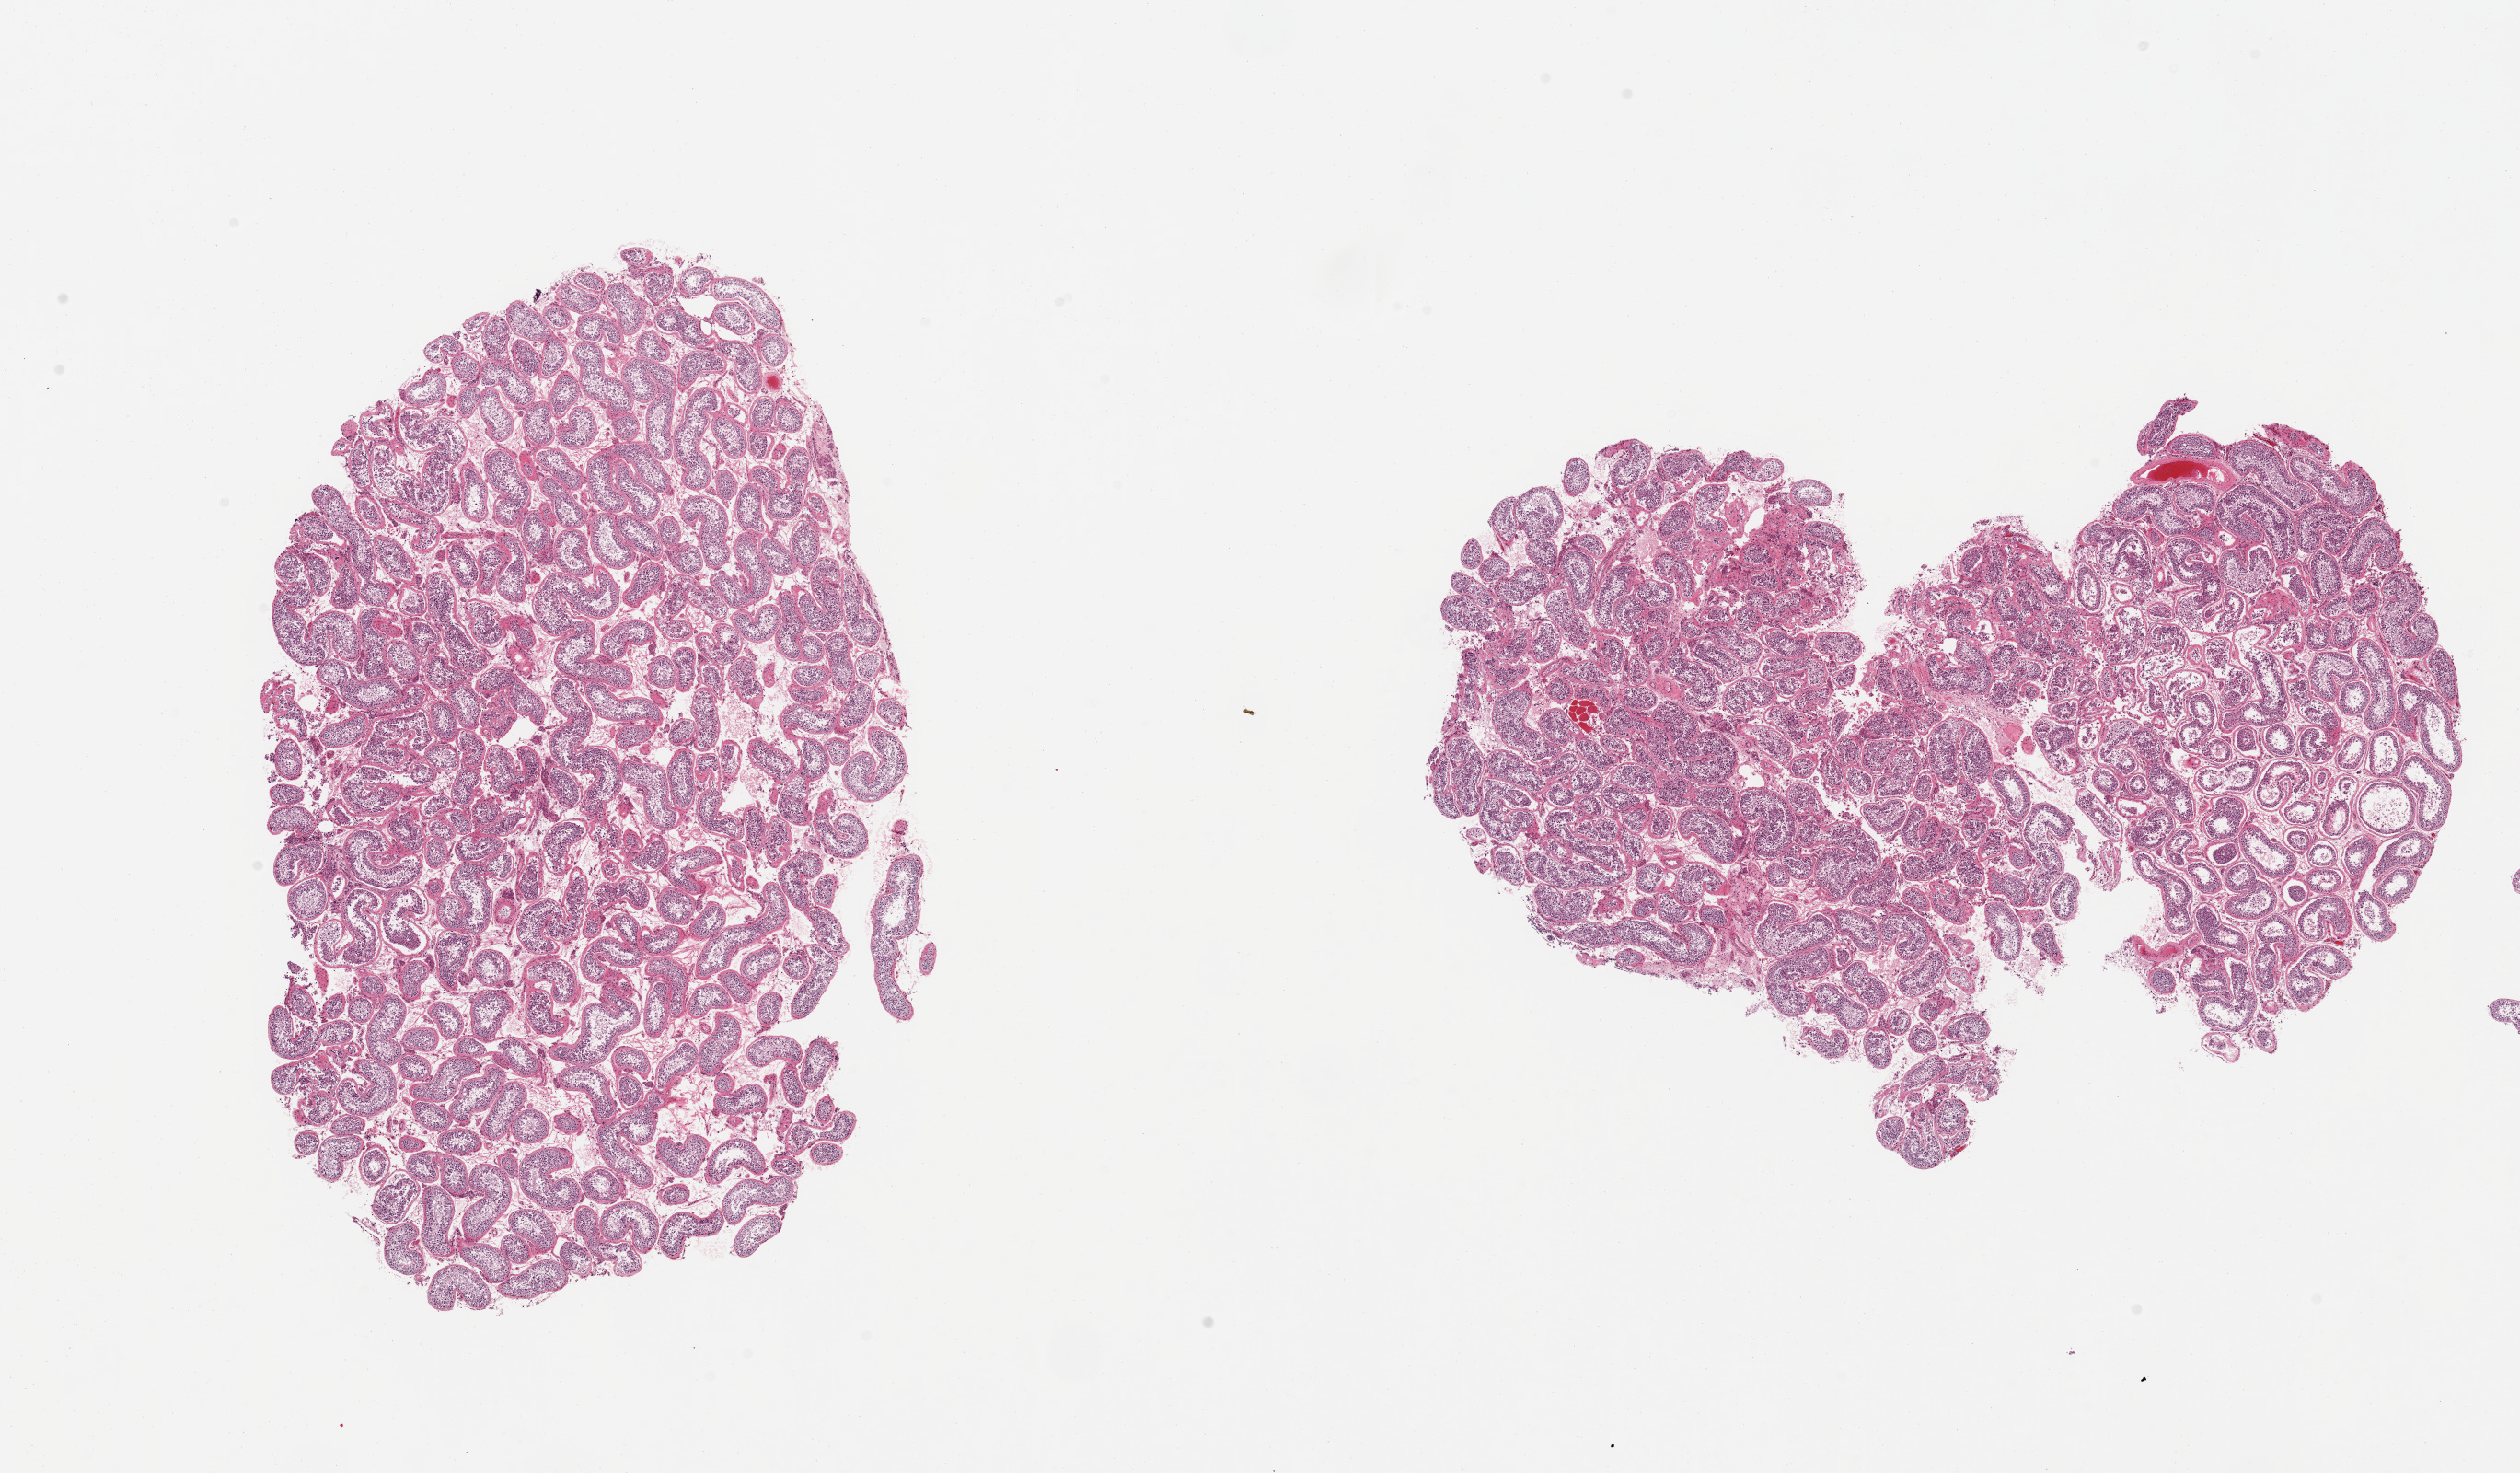
H&E whole-slide image — a low-resolution overview of the entire scanned area, about 21.7 x 12.7 mm; PAXgene-fixed, paraffin-embedded tissue; target tissue: testis; tissue donor sample.
Pathologist's review note for this sample: 2 pieces; spermatogenesis present but possibly reduced.